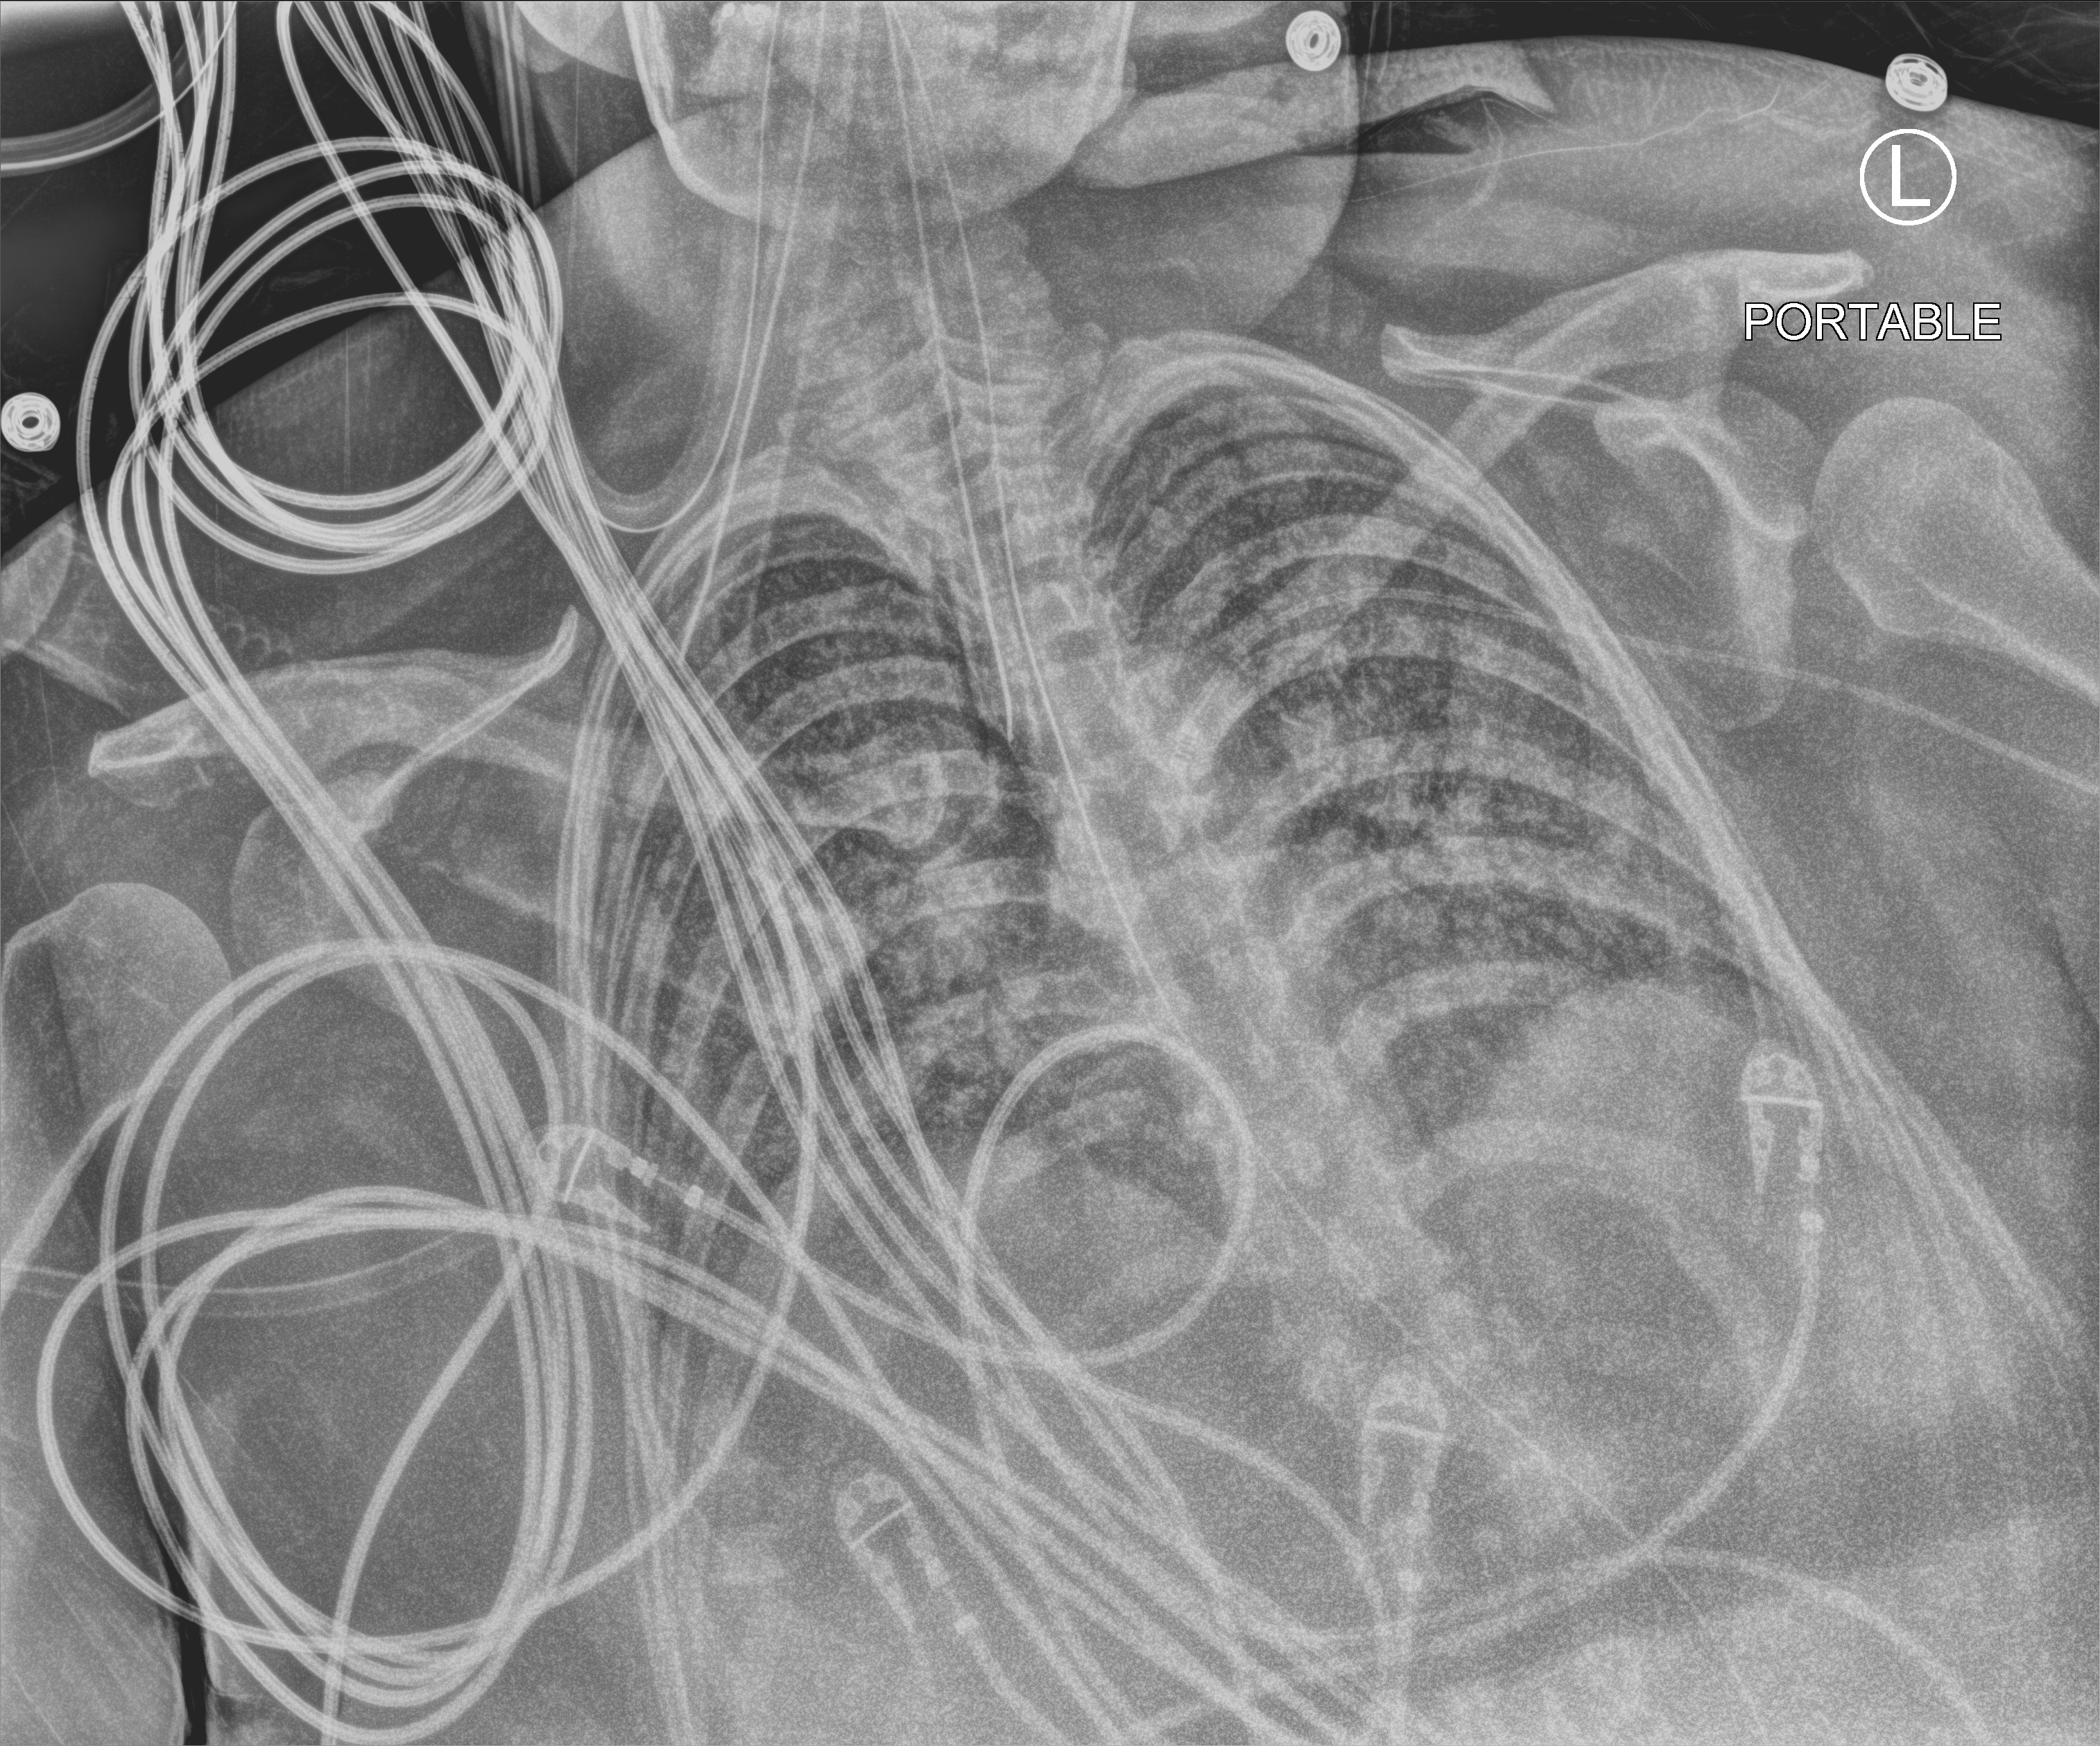
Portable chest radiograph, anteroposterior (AP) projection. Patient hospitalised with COVID-19; female, aged 18–59 years.
Admission-level facts for this patient (not findings on this image; timing relative to this image not recorded):
- admitted to intensive care during this hospital stay: yes